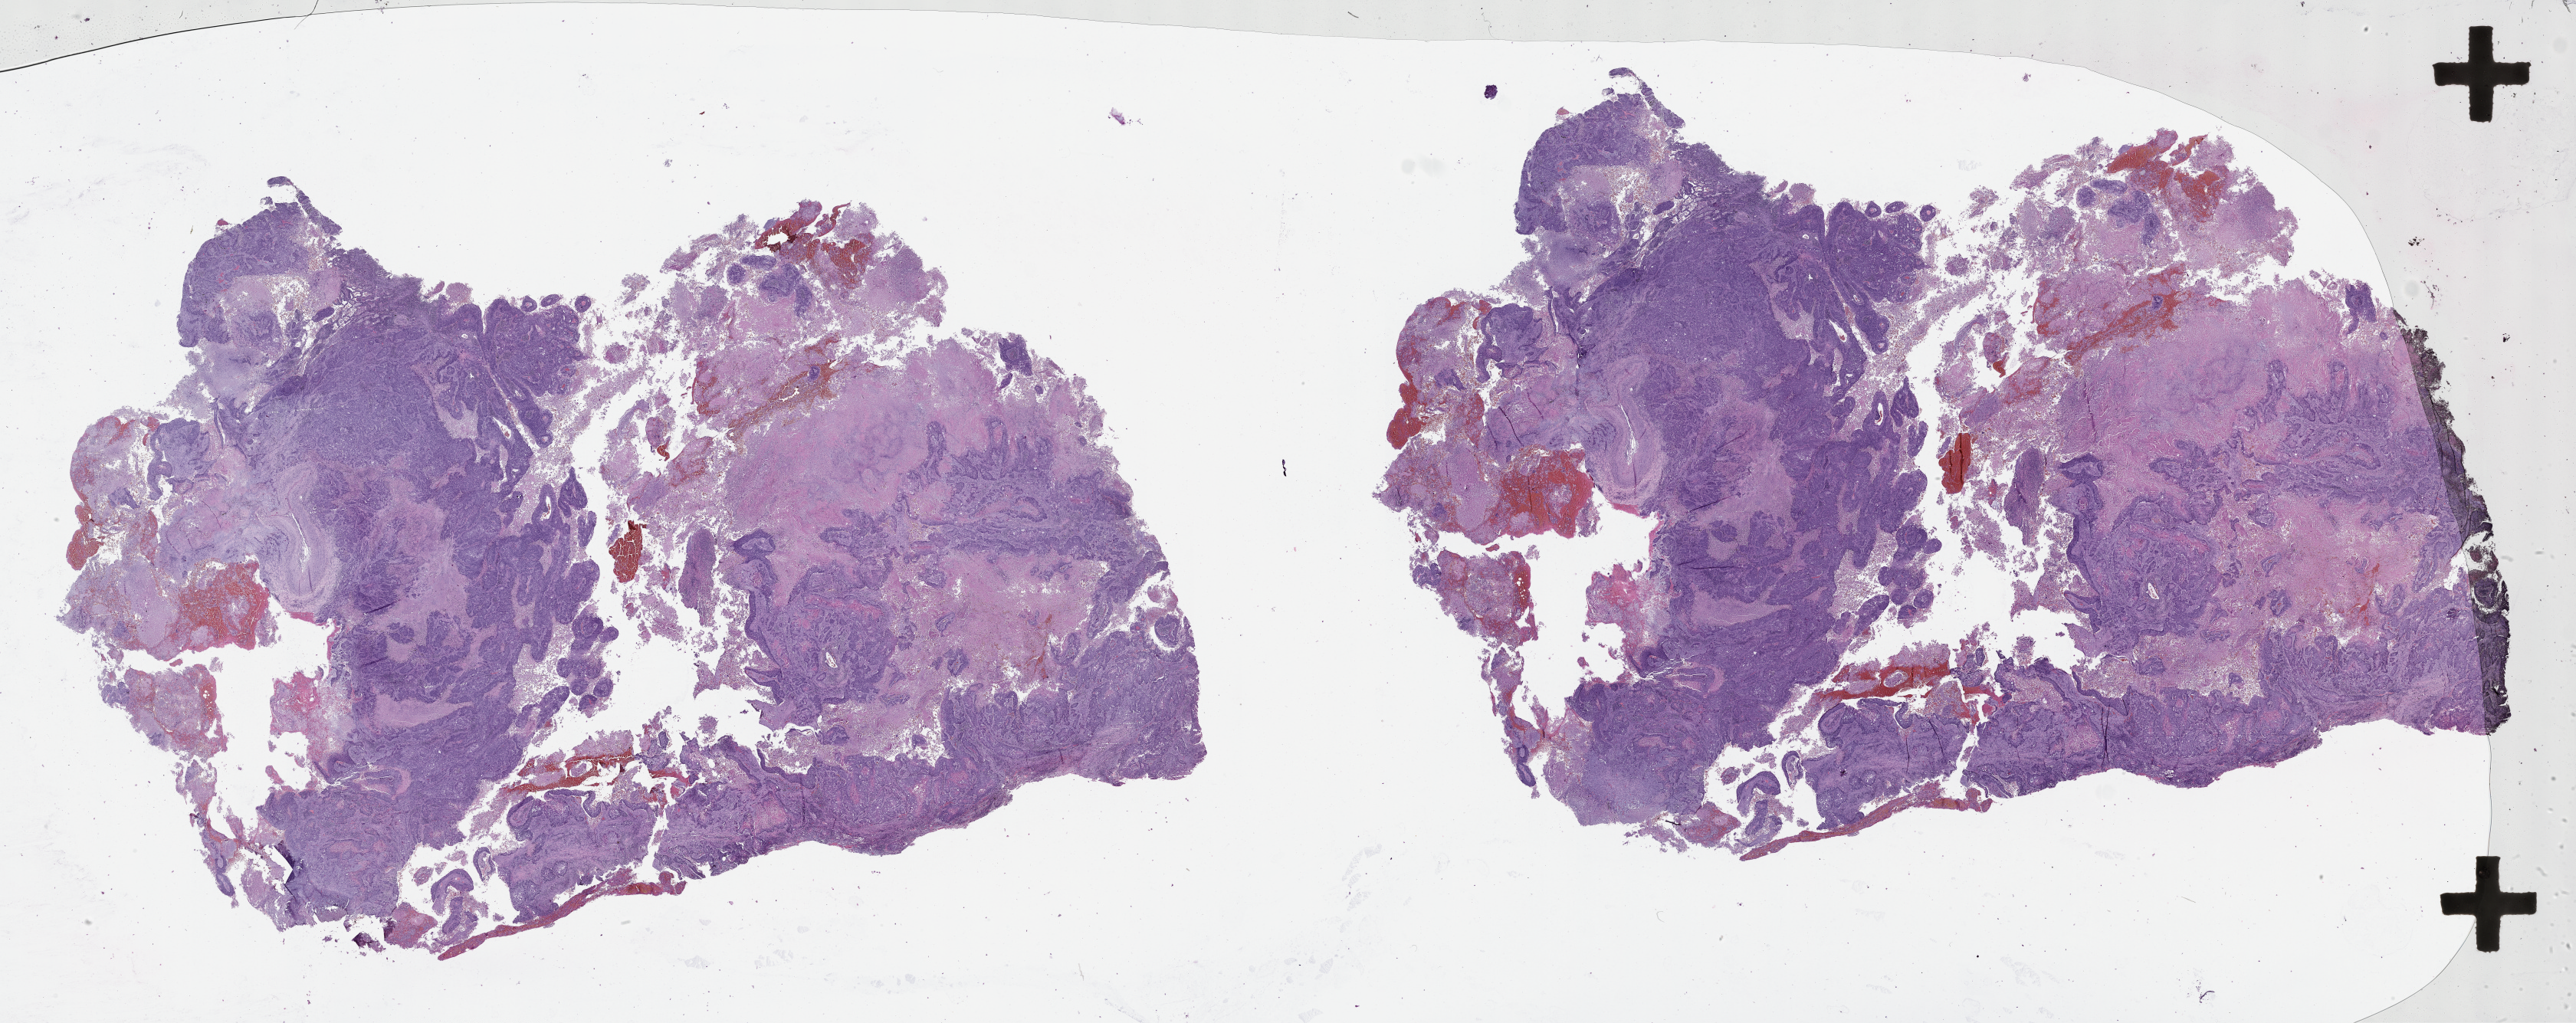
H&E whole-slide image — whole scanned area (about 54.1 x 21.5 mm, from a 20x scan) shown as a low-resolution overview, tumour tissue sample, lung. Male, 57 y/o.
Patient diagnosis (cohort enrolment): squamous cell carcinoma (lung).